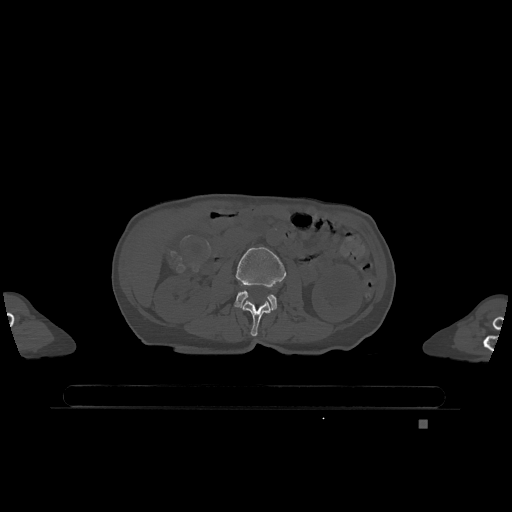
CT including the spine, one axial slice. Slice 385 of 1317 in the series (ordered by position). Bone window (W 1800 / L 400 HU). 0.5 mm slice thickness. 512 × 512 image matrix. Female patient, age 74 years. Case-level facts recorded for this patient, not image findings: primary cancer: lung; vertebrae with lytic lesions (as recorded): T1, T4, T5, T6, L4, L5.
Outlined on this slice (semi-automatically segmented with operator editing):
- L2 vertebra: bounding box <242,301,271,337> (left, top, right, bottom; pixels)
- L3 vertebra: <234,247,286,311>